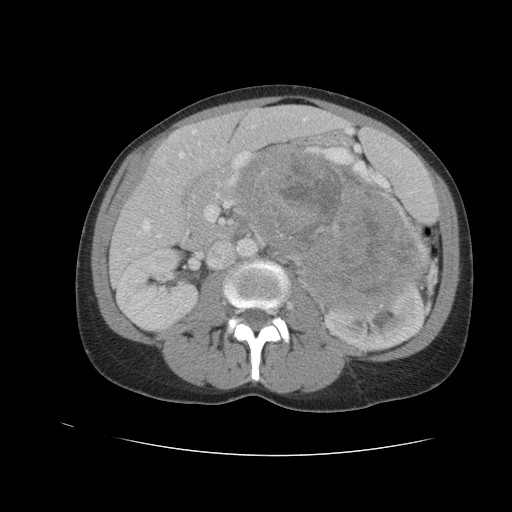
Contrast-enhanced abdominal CT, one axial slice; slice 55 of 90 in the series (ordered by position); 120 kVp; intravenous contrast given; soft-tissue window (W 400 / L 40 HU); 512 × 512 image matrix, field of view 360 × 360 mm. Female patient. From the clinical record (not read from this slice): diagnosis: adrenocortical carcinoma; tumour side: left adrenal; tumour size at pathology: 18 cm; Ki-67 index: 11 %.
Structures marked on this image (semi-automatic segmentation, software-assisted and operator-edited):
- mass: box from (x=245, y=150) to (x=421, y=307) px